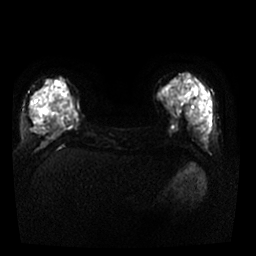
Breast MRI, one axial slice; position 8 of 29 along the scan axis; diffusion-weighted series; image 2 of 4 stored at this slice position (different b-values; order by instance number); 1.5 T; 4 mm slice thickness; 256 × 256 image matrix, field of view 340 × 340 mm. Female patient.
Annotated regions visible in this slice (expert manual segmentation):
- tumour on diffusion-weighted imaging: bounding box (x1, y1, x2, y2) in pixels: (73, 114, 77, 118)